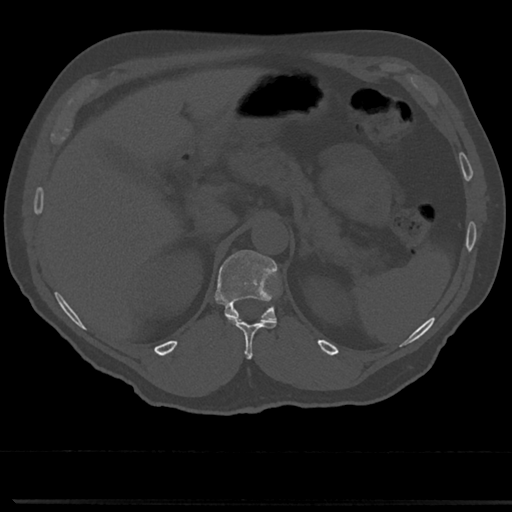
CT including the spine, one axial slice; slice 172 of 817 in the series (ordered by position); reconstruction kernel Br40s/3; 120 kVp; bone window (W 1800 / L 400 HU); 512 × 512 image matrix. Patient: male, 61 years. Case-level facts recorded for this patient, not image findings: primary cancer: prostate.
Annotated regions visible in this slice (semi-automatic segmentation, software-assisted and operator-edited):
- T11 vertebra: box from (x=242, y=322) to (x=273, y=358) px
- T12 vertebra: (x=214, y=250)–(x=285, y=336)